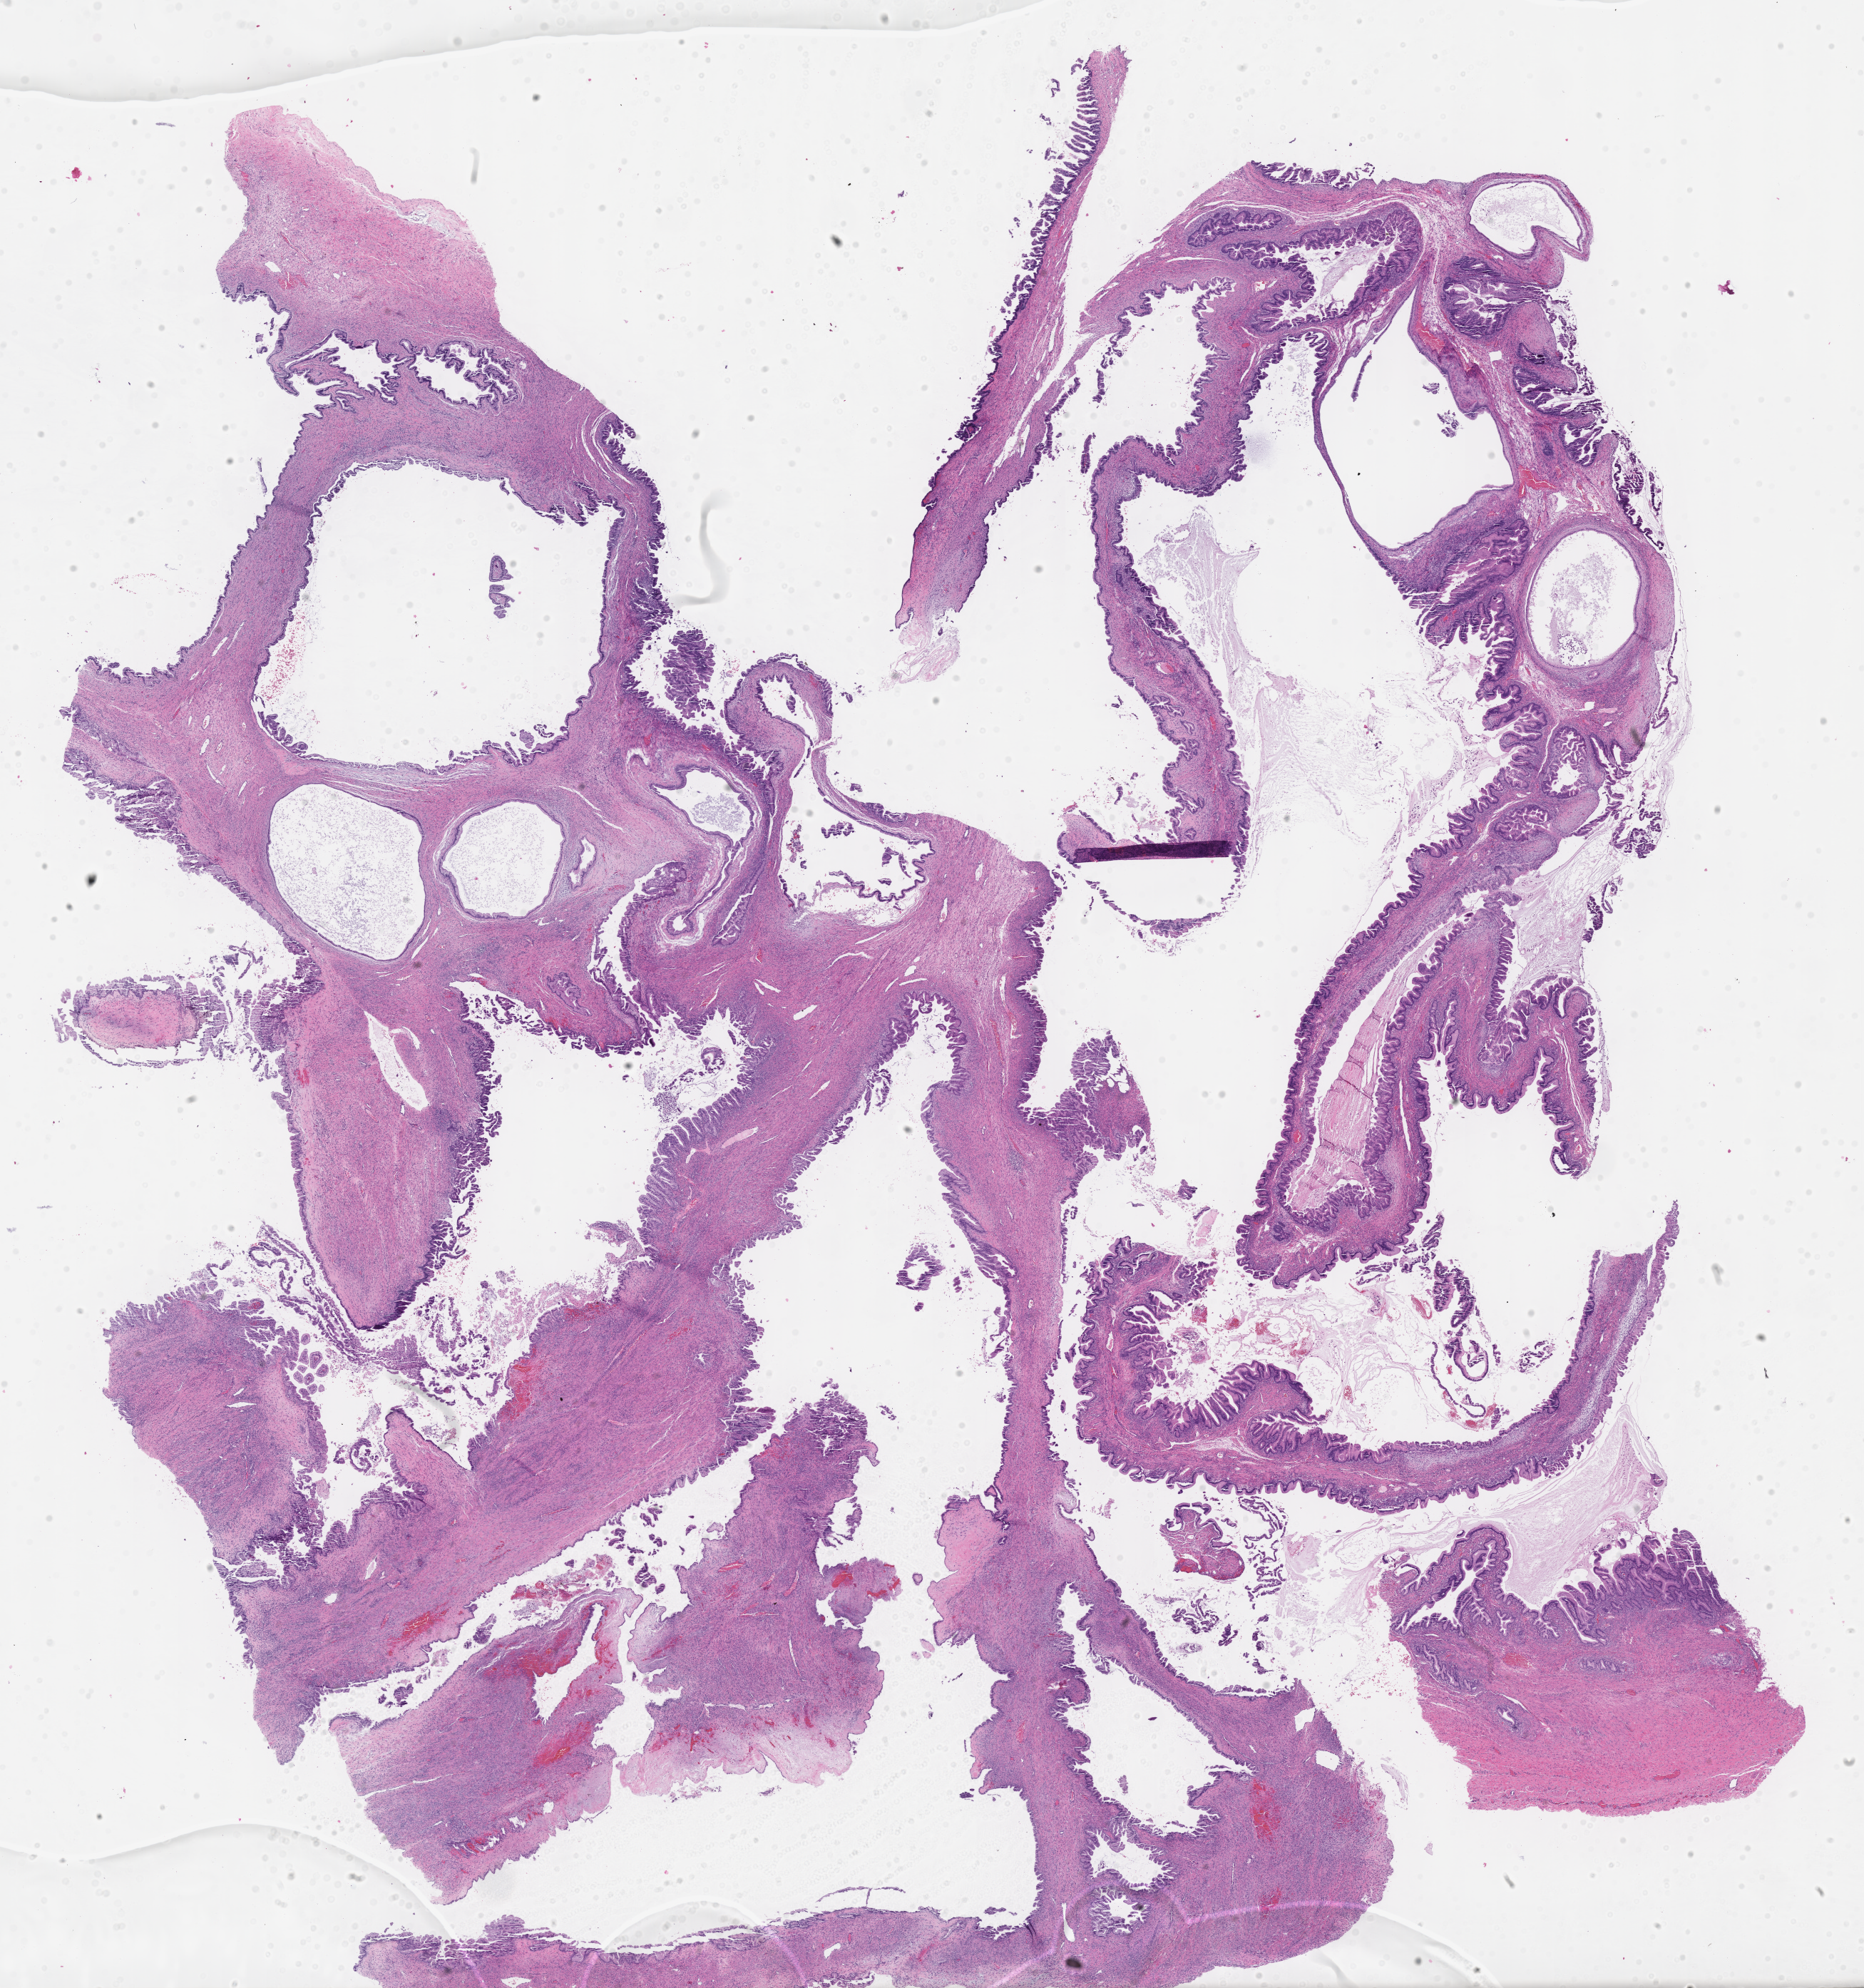
Digitized H&E-stained section, shown as a low-resolution overview of the whole scanned area (about 21.1 x 22.5 mm). Formalin-fixed paraffin-embedded section. Primary tumor. Anatomic site: ovary. Female patient; age at initial diagnosis 72 years. Composition of this section per pathologist review: tumor cells 30%, tumor nuclei 40%, stromal cells 70%, necrosis 0%, normal cells 0%. Infiltration values recorded for this section: lymphocyte infiltration 0%, monocyte infiltration 0%, neutrophil infiltration 0%.
- diagnosis: Mucinous adenocarcinoma
- FIGO stage: Stage IC2